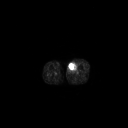
FDG PET of an extremity soft-tissue mass (from a PET/CT study), one axial slice. Slice 211 of 267 in the series (ordered by position). 3.27 mm slice thickness. 128 × 128 image matrix, field of view 700 × 700 mm. Male patient, age 48 years. From the clinical record (not read from this slice): histological type: pleiomorphic leiomyosarcoma; grade: high; site of the primary tumour: left thigh.
Structures marked on this image (expert contour drawn on MRI and transferred to this co-registered scan by the dataset authors):
- gross tumour volume including surrounding oedema: box from (x=69, y=63) to (x=77, y=73) px
- gross tumour volume (mass): (x=69, y=63)–(x=77, y=71)